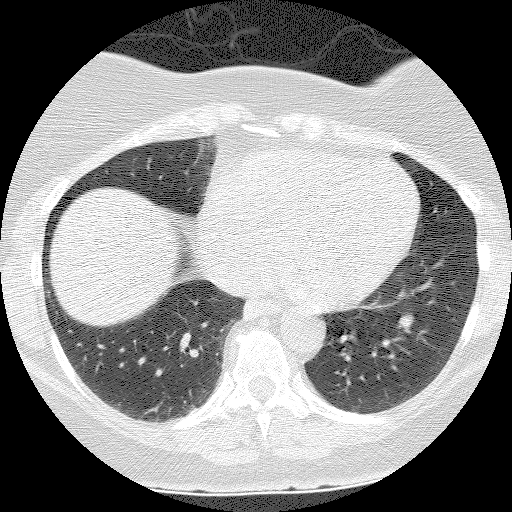
Axial slice from a low-dose chest CT screening exam. Second annual screen. Lung window (W 1500 / L -600 HU). Lung (sharp) reconstruction kernel (BONE). 120 kVp. Slice 91 of 140 in the series. Female, age 55 years at enrolment. Former smoker at enrolment.
Expert-annotated lung lesion, bounding box (x1, y1, x2, y2) in pixels: (383, 304, 427, 346). The screening reader recorded 3 non-calcified nodules or masses ≥4 mm on this exam (left lower lobe, right lower lobe, right lower lobe); which of them this box marks is not recorded. Official screen result: positive, no significant change: stable abnormalities potentially related to lung cancer, unchanged since the prior screening exam. Later outcome: lung cancer diagnosed 655 days after this screen (after the third annual screen) — carcinoid tumor, NOS, left lower lobe, carcinoid, stage not assessed, 10 mm at pathology.